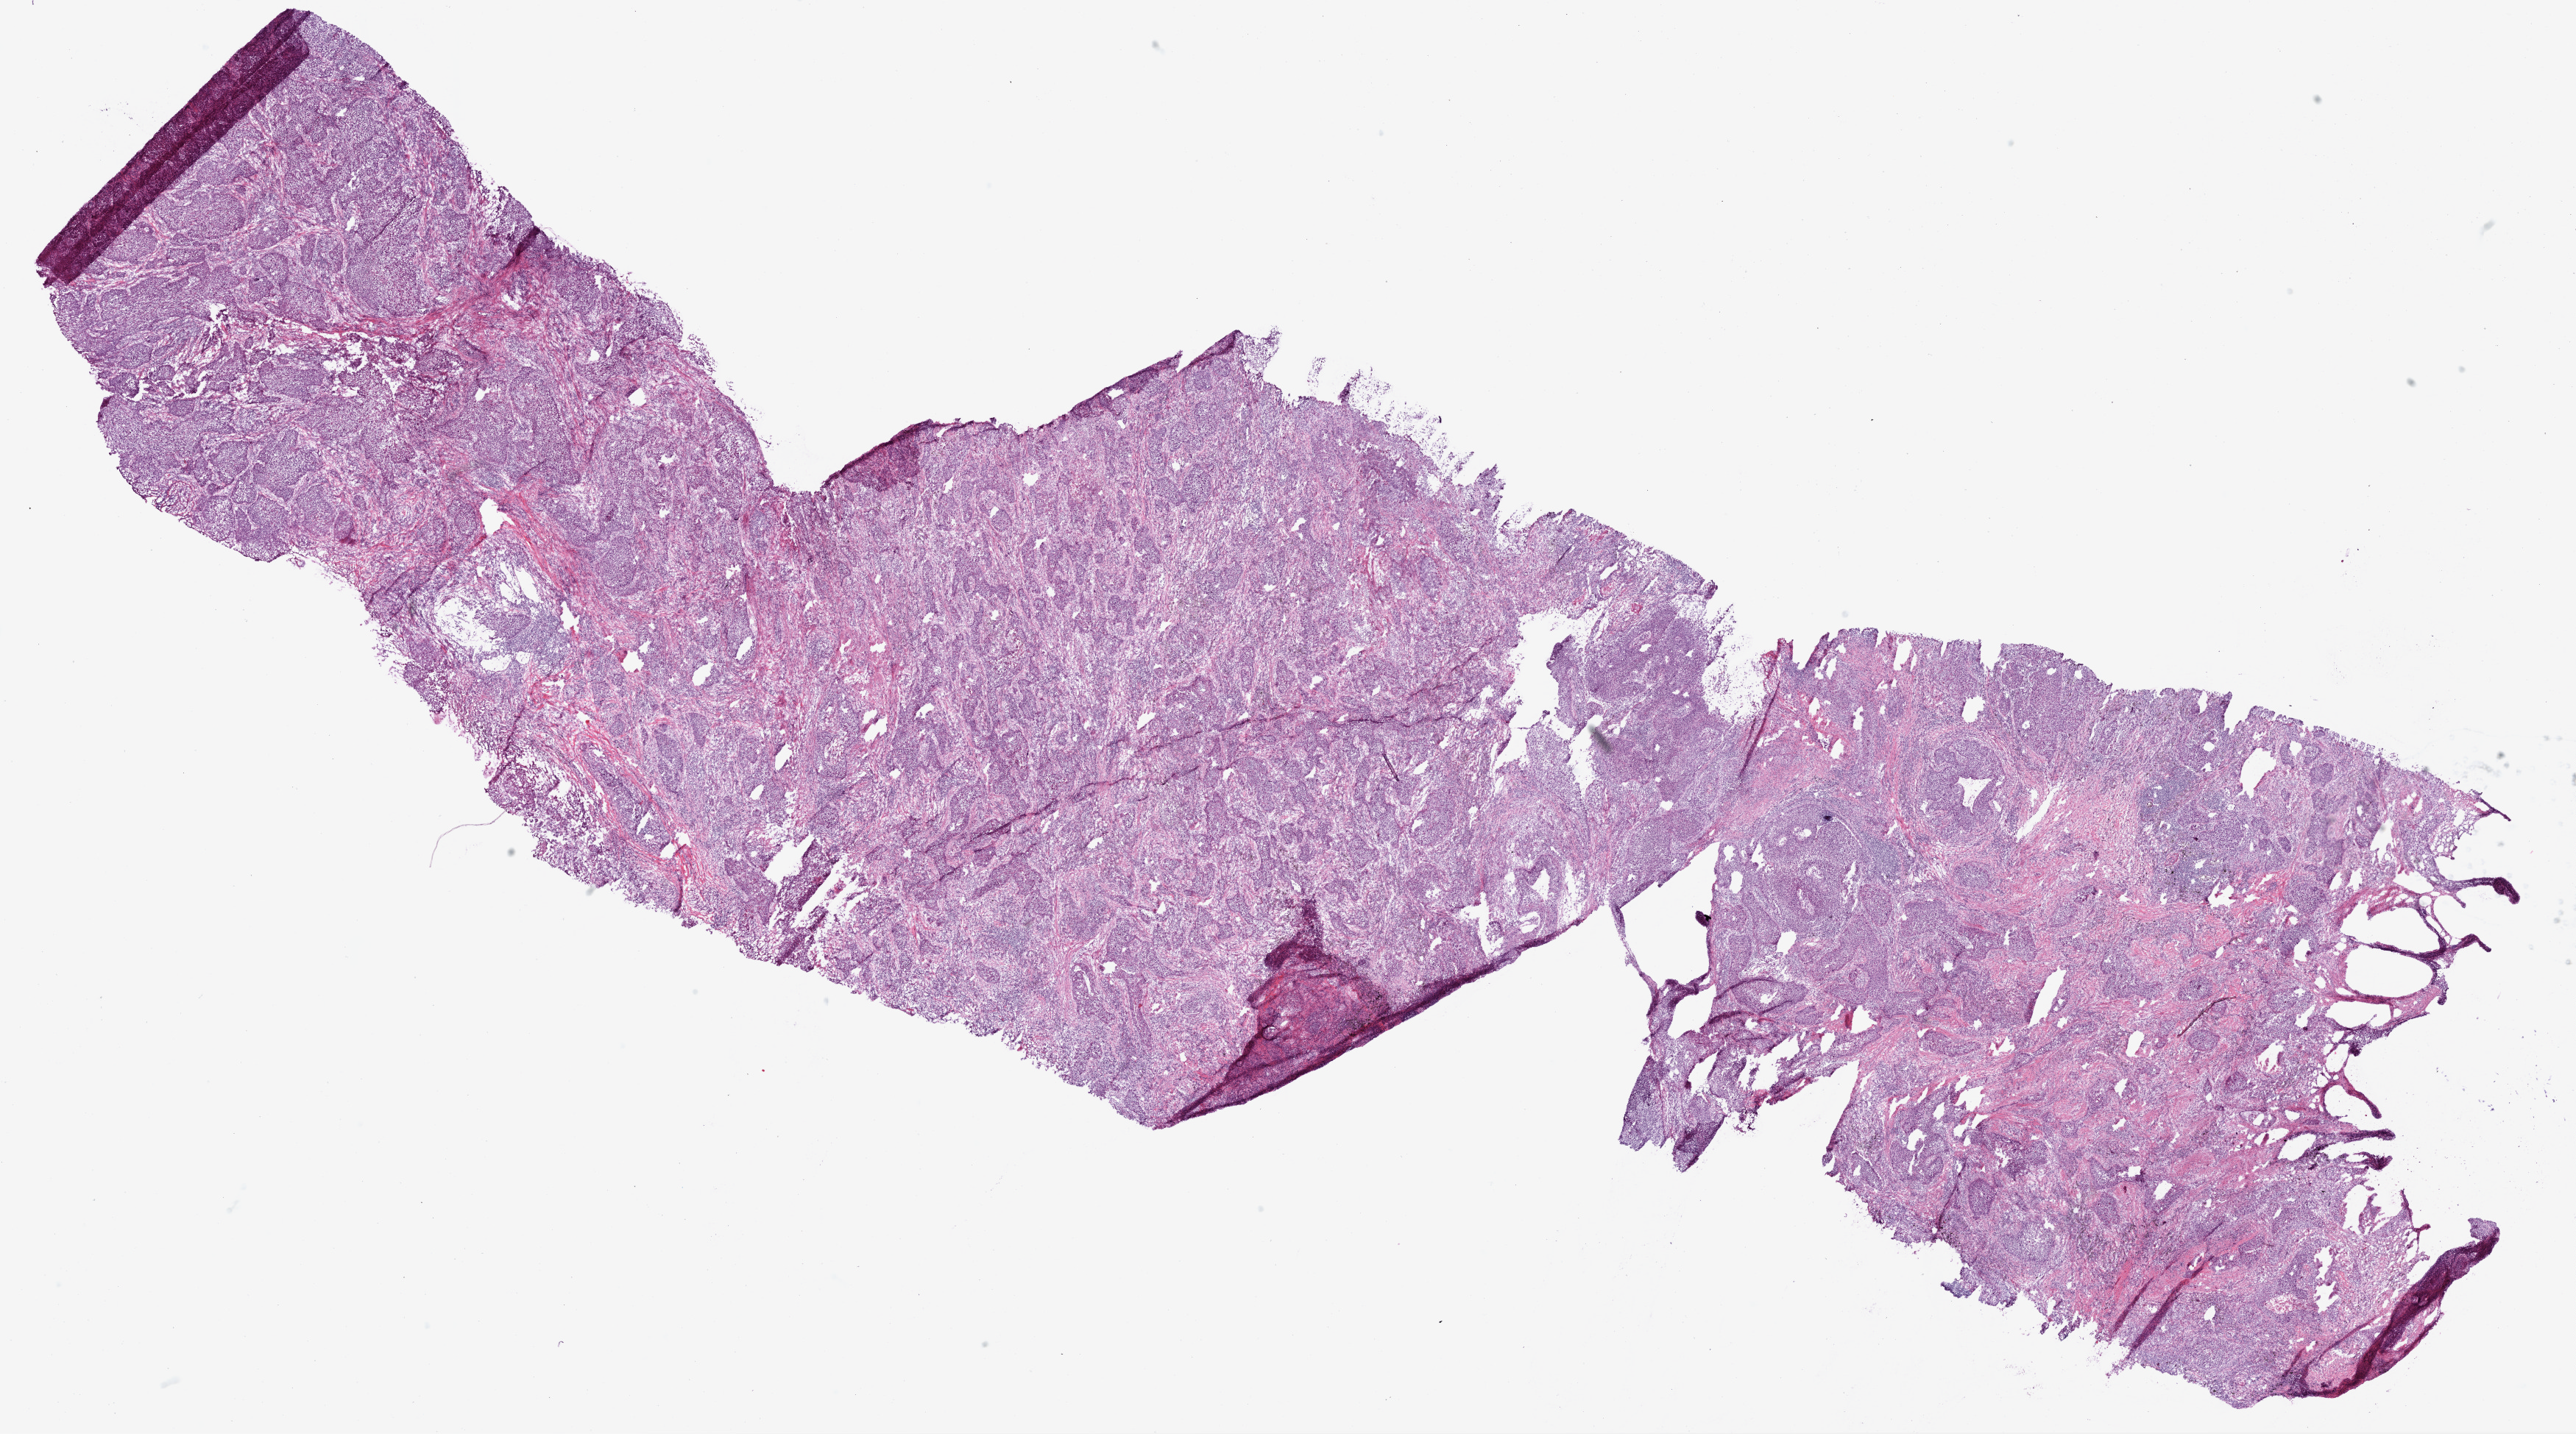
H&E whole-slide image, a low-resolution overview of the entire scanned area, about 28.1 x 15.6 mm (from a 20x scan); frozen section from the top of the tissue portion; sample: primary tumour, lung. Male, age 71 years at initial diagnosis.
Pathologic diagnosis: Squamous cell carcinoma, NOS (upper lobe, lung).